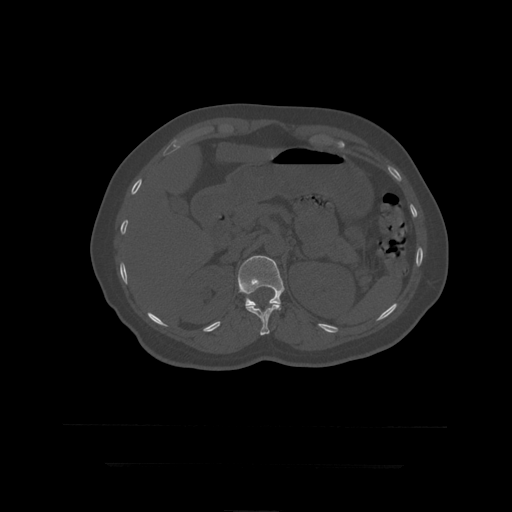
CT including the spine, one axial slice; reconstruction kernel STANDARD; bone window (W 1800 / L 400 HU); 512 × 512 image matrix. Patient age 41 years. From the clinical record (not read from this slice): primary cancer: breast.
Structures marked on this image (semi-automatic segmentation, software-assisted and operator-edited):
- L1 vertebra: bounding box [x1, y1, x2, y2] px = [238, 256, 285, 311]
- T12 vertebra: [246, 303, 281, 336]